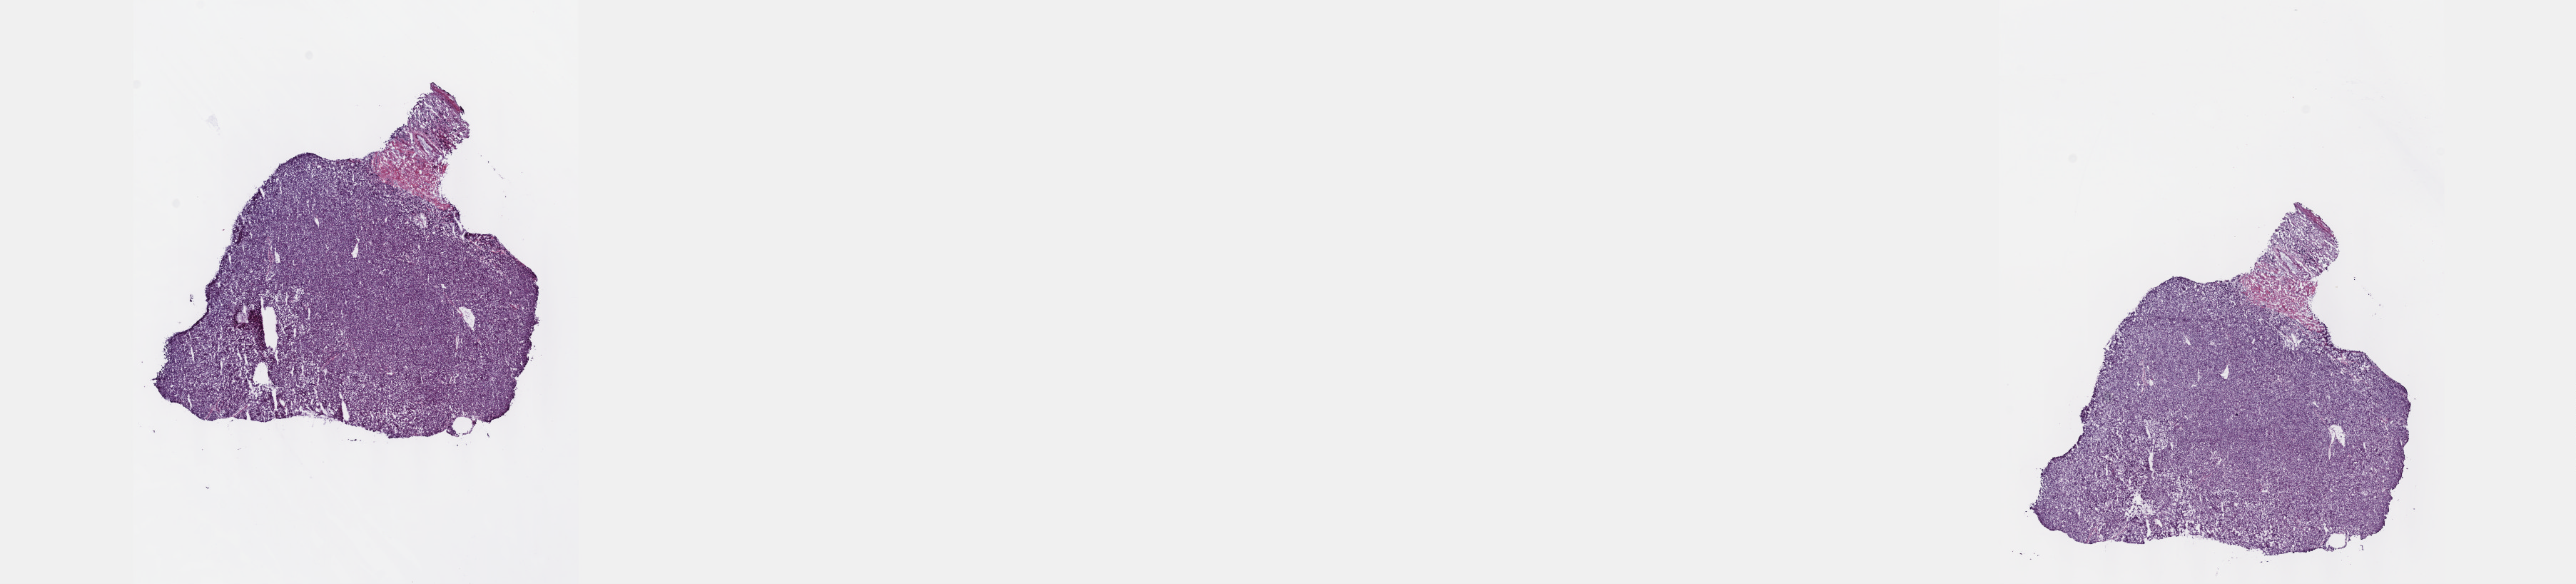
H&E whole-slide image — whole scanned area (about 29.2 x 6.6 mm, from a 40x scan) shown as a low-resolution overview. Frozen section from the top of the tissue portion. Liver, primary tumour sample. Female patient; age at initial diagnosis 67 years. Histologic grade: G1 (well differentiated). Pathologist review of this section (percent, as recorded): tumour cells 95%, tumour nuclei 90%, normal cells 0%, stromal cells 5%, necrosis 0%. Inflammatory infiltration, as recorded: lymphocyte infiltration 0%, monocyte infiltration 0%, neutrophil infiltration 0%.
Histologic diagnosis: Hepatocellular carcinoma, NOS.